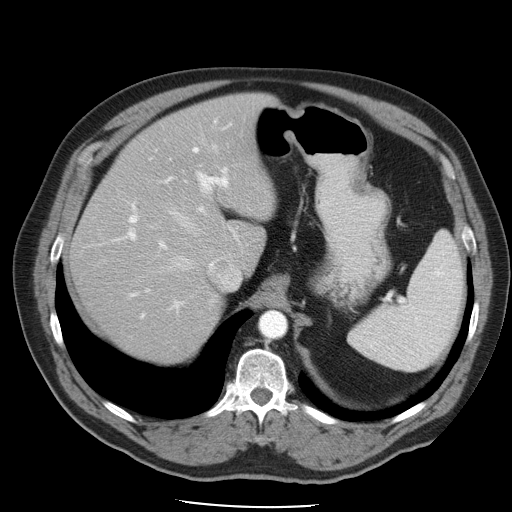
Contrast-enhanced abdominal CT, one axial slice. Reconstruction kernel STANDARD. 120 kVp. Intravenous contrast given. Soft-tissue window (W 400 / L 40 HU). 5 mm slice thickness. 512 × 512 image matrix. Male patient, age 68 years. Case-level facts recorded for this patient, not image findings: diagnosis: colorectal cancer liver metastases, imaged before liver resection; multiple liver metastases: yes; largest metastasis: 1.7 cm; disease in both lobes: no.
Outlined on this slice (expert manual segmentation):
- hepatic veins: bounding box (x1, y1, x2, y2) in pixels: (156, 145, 241, 289)
- liver: (71, 96, 272, 361)
- planned liver remnant (the part of the liver to remain after resection): (71, 96, 272, 361)
- portal vein (with intrahepatic branches): (102, 121, 232, 319)